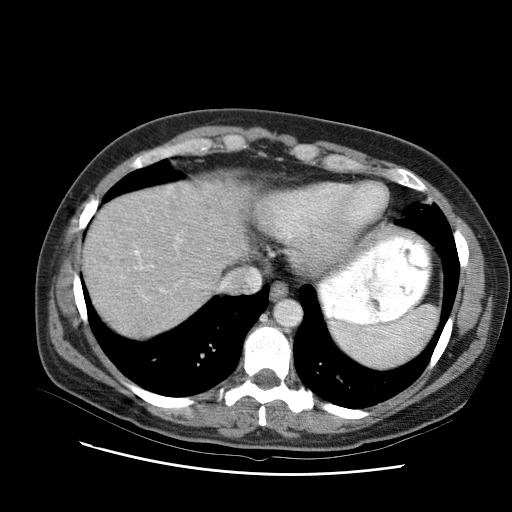
Contrast-enhanced abdominal CT (liver protocol), one axial slice. Position 82 of 95 along the scan axis. Reconstruction kernel STANDARD. 120 kVp. One of 2 acquisitions stored at this slice position. Soft-tissue window (W 400 / L 40 HU). 512 × 512 image matrix, field of view 360 × 360 mm. From the clinical record (not read from this slice): diagnosis: hepatocellular carcinoma (patient treated with transarterial chemoembolisation; whether this scan precedes or follows treatment is not stated here); TNM stage (as recorded): Stage-I; Child-Pugh class: B; tumour differentiation: moderately differentiated.
Outlined on this slice (semi-automatically segmented with operator editing):
- liver parenchyma outside the tumour (the mass and vessels are separate outlines, so this box may not span the whole liver): box from (x=88, y=188) to (x=228, y=314) px
- liver vessels: (x=134, y=237)–(x=137, y=240)